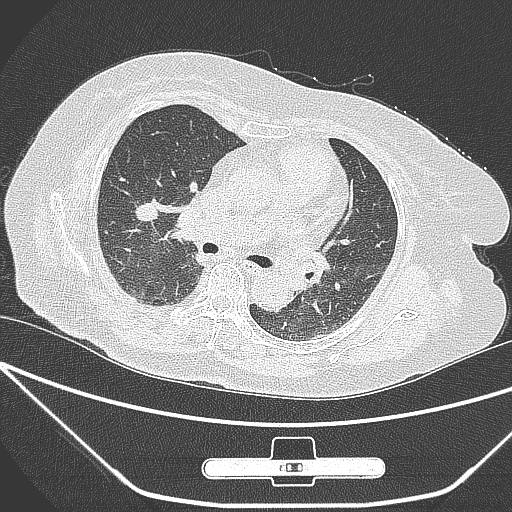
Chest CT, one axial slice. Position 157 of 245 along the scan axis. Lung window (W 1500 / L -600 HU). 512 × 512 image matrix. Female patient, age 65 years. Case-level facts recorded for this patient, not image findings: clinical TNM (as recorded): T1c N0 M0; histopathological grade: G3.
Outlined on this slice (rectangle marked by the reading radiologist):
- lung tumour (recorded histology: adenocarcinoma): box from (x=126, y=196) to (x=169, y=230) px